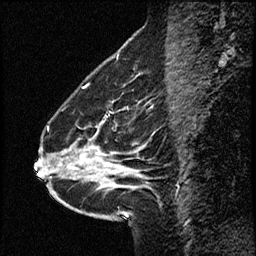
Breast MRI (dynamic contrast-enhanced), one sagittal slice. Slice 22 of 50 in the series (ordered by position). Dynamic contrast-enhanced study with each time point stored as its own series, time point 2 of 4 at this slice position (early post-contrast, ordered by acquisition time). 1.5 T. TE 4.2 ms, TR 17.5 ms. 3 mm slice thickness. 256 × 256 image matrix. From the clinical record (not read from this slice): setting: breast cancer imaged before/during neoadjuvant chemotherapy.
Structures marked on this image (semi-automatic segmentation, software-assisted and operator-edited):
- analysis volume of interest (the breast-tissue region the enhancement analysis was run in; not a lesion): box from (x=52, y=98) to (x=158, y=207) px
- tumour enhancement mask (voxels above the 100 % enhancement threshold inside the analysis volume of interest): (x=81, y=157)–(x=118, y=172)